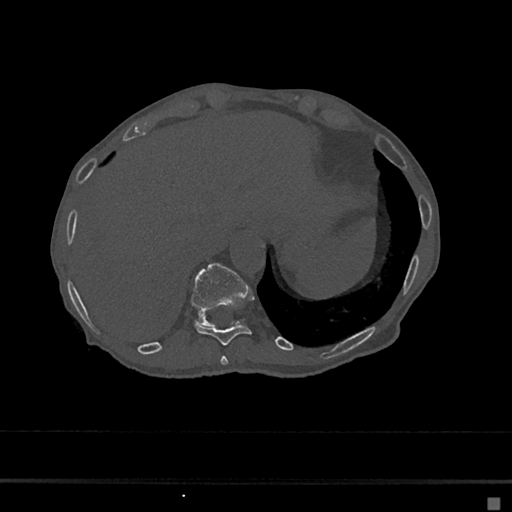
CT including the spine, one axial slice. Position 209 of 797 along the scan axis. Reconstruction kernel Br40s/3. Bone window (W 1800 / L 400 HU). 512 × 512 image matrix. Female patient, age 68 years. Case-level facts recorded for this patient, not image findings: primary cancer: renal.
Structures marked on this image (semi-automatic segmentation, software-assisted and operator-edited):
- T10 vertebra: bounding box [x1, y1, x2, y2] px = [195, 324, 252, 346]
- T11 vertebra: [191, 263, 249, 326]
- T9 vertebra: [220, 356, 228, 366]